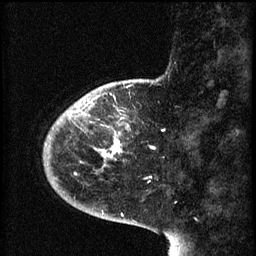
Breast MRI (dynamic contrast-enhanced), one sagittal slice; position 13 of 60 along the scan axis; 3 images stored at this slice position (order not interpretable as contrast timing); 1.5 T; TE 4.2 ms, TR 8.1 ms; 256 × 256 image matrix, field of view 200 × 200 mm. Patient: female, 44 years.
Outlined on this slice (semi-automatically segmented with operator editing):
- analysis volume of interest (the breast-tissue region the enhancement analysis was run in; not a lesion): bounding box <59,110,138,167> (left, top, right, bottom; pixels)
- tumour enhancement mask (voxels above the 70 % enhancement threshold inside the analysis volume of interest): <69,110,122,167>